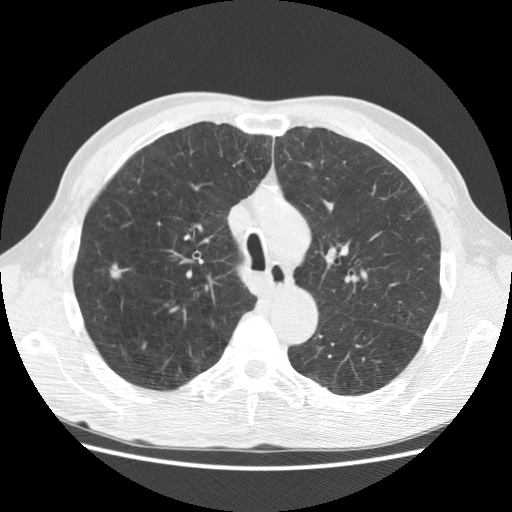
Low-dose screening chest CT, axial slice; baseline annual screen; lung window (W 1500 / L -600 HU); standard (soft-tissue) reconstruction kernel (STANDARD). Male, age 62 years at enrolment. Current smoker at enrolment.
Expert-annotated lung lesion, box from (x=102, y=260) to (x=135, y=291) px. The screening reader recorded 2 non-calcified nodules or masses ≥4 mm on this exam; which of them this box marks is not recorded.